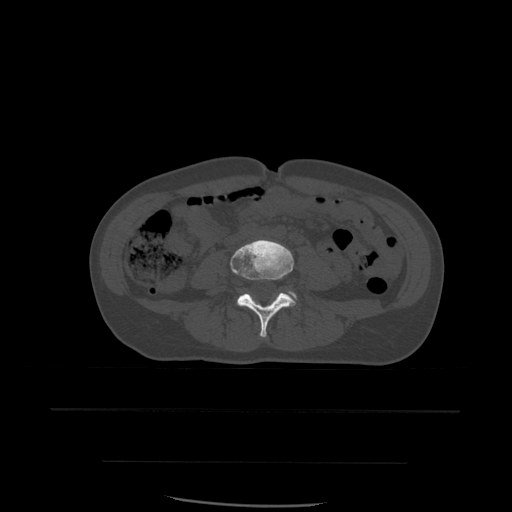
CT including the spine, one axial slice; position 167 of 574 along the scan axis; bone window (W 1800 / L 400 HU); 1.25 mm slice thickness; 512 × 512 image matrix, field of view 392 × 392 mm. Patient age 48 years. Case-level facts recorded for this patient, not image findings: primary cancer: lung; vertebrae with lytic lesions (as recorded): T11.
Annotated regions visible in this slice (semi-automatically segmented with operator editing):
- L4 vertebra: bounding box [x1, y1, x2, y2] px = [231, 240, 296, 338]
- L5 vertebra: [238, 292, 297, 302]